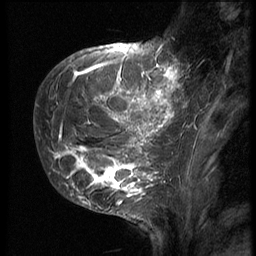
Breast MRI (dynamic contrast-enhanced), one sagittal slice. Slice 16 of 62 in the series (ordered by position). 3 images stored at this slice position (order not interpretable as contrast timing). 1.5 T. TE 4.2 ms, TR 9 ms. 2.5 mm slice thickness. 256 × 256 image matrix. Female patient, age 28 years. Case-level facts recorded for this patient, not image findings: setting: breast cancer imaged before/during neoadjuvant chemotherapy.
Annotated regions visible in this slice (semi-automatically segmented with operator editing):
- analysis volume of interest (the breast-tissue region the enhancement analysis was run in; not a lesion): bounding box [x1, y1, x2, y2] px = [42, 57, 192, 207]
- tumour enhancement mask (voxels above the 140 % enhancement threshold inside the analysis volume of interest): [52, 61, 184, 205]